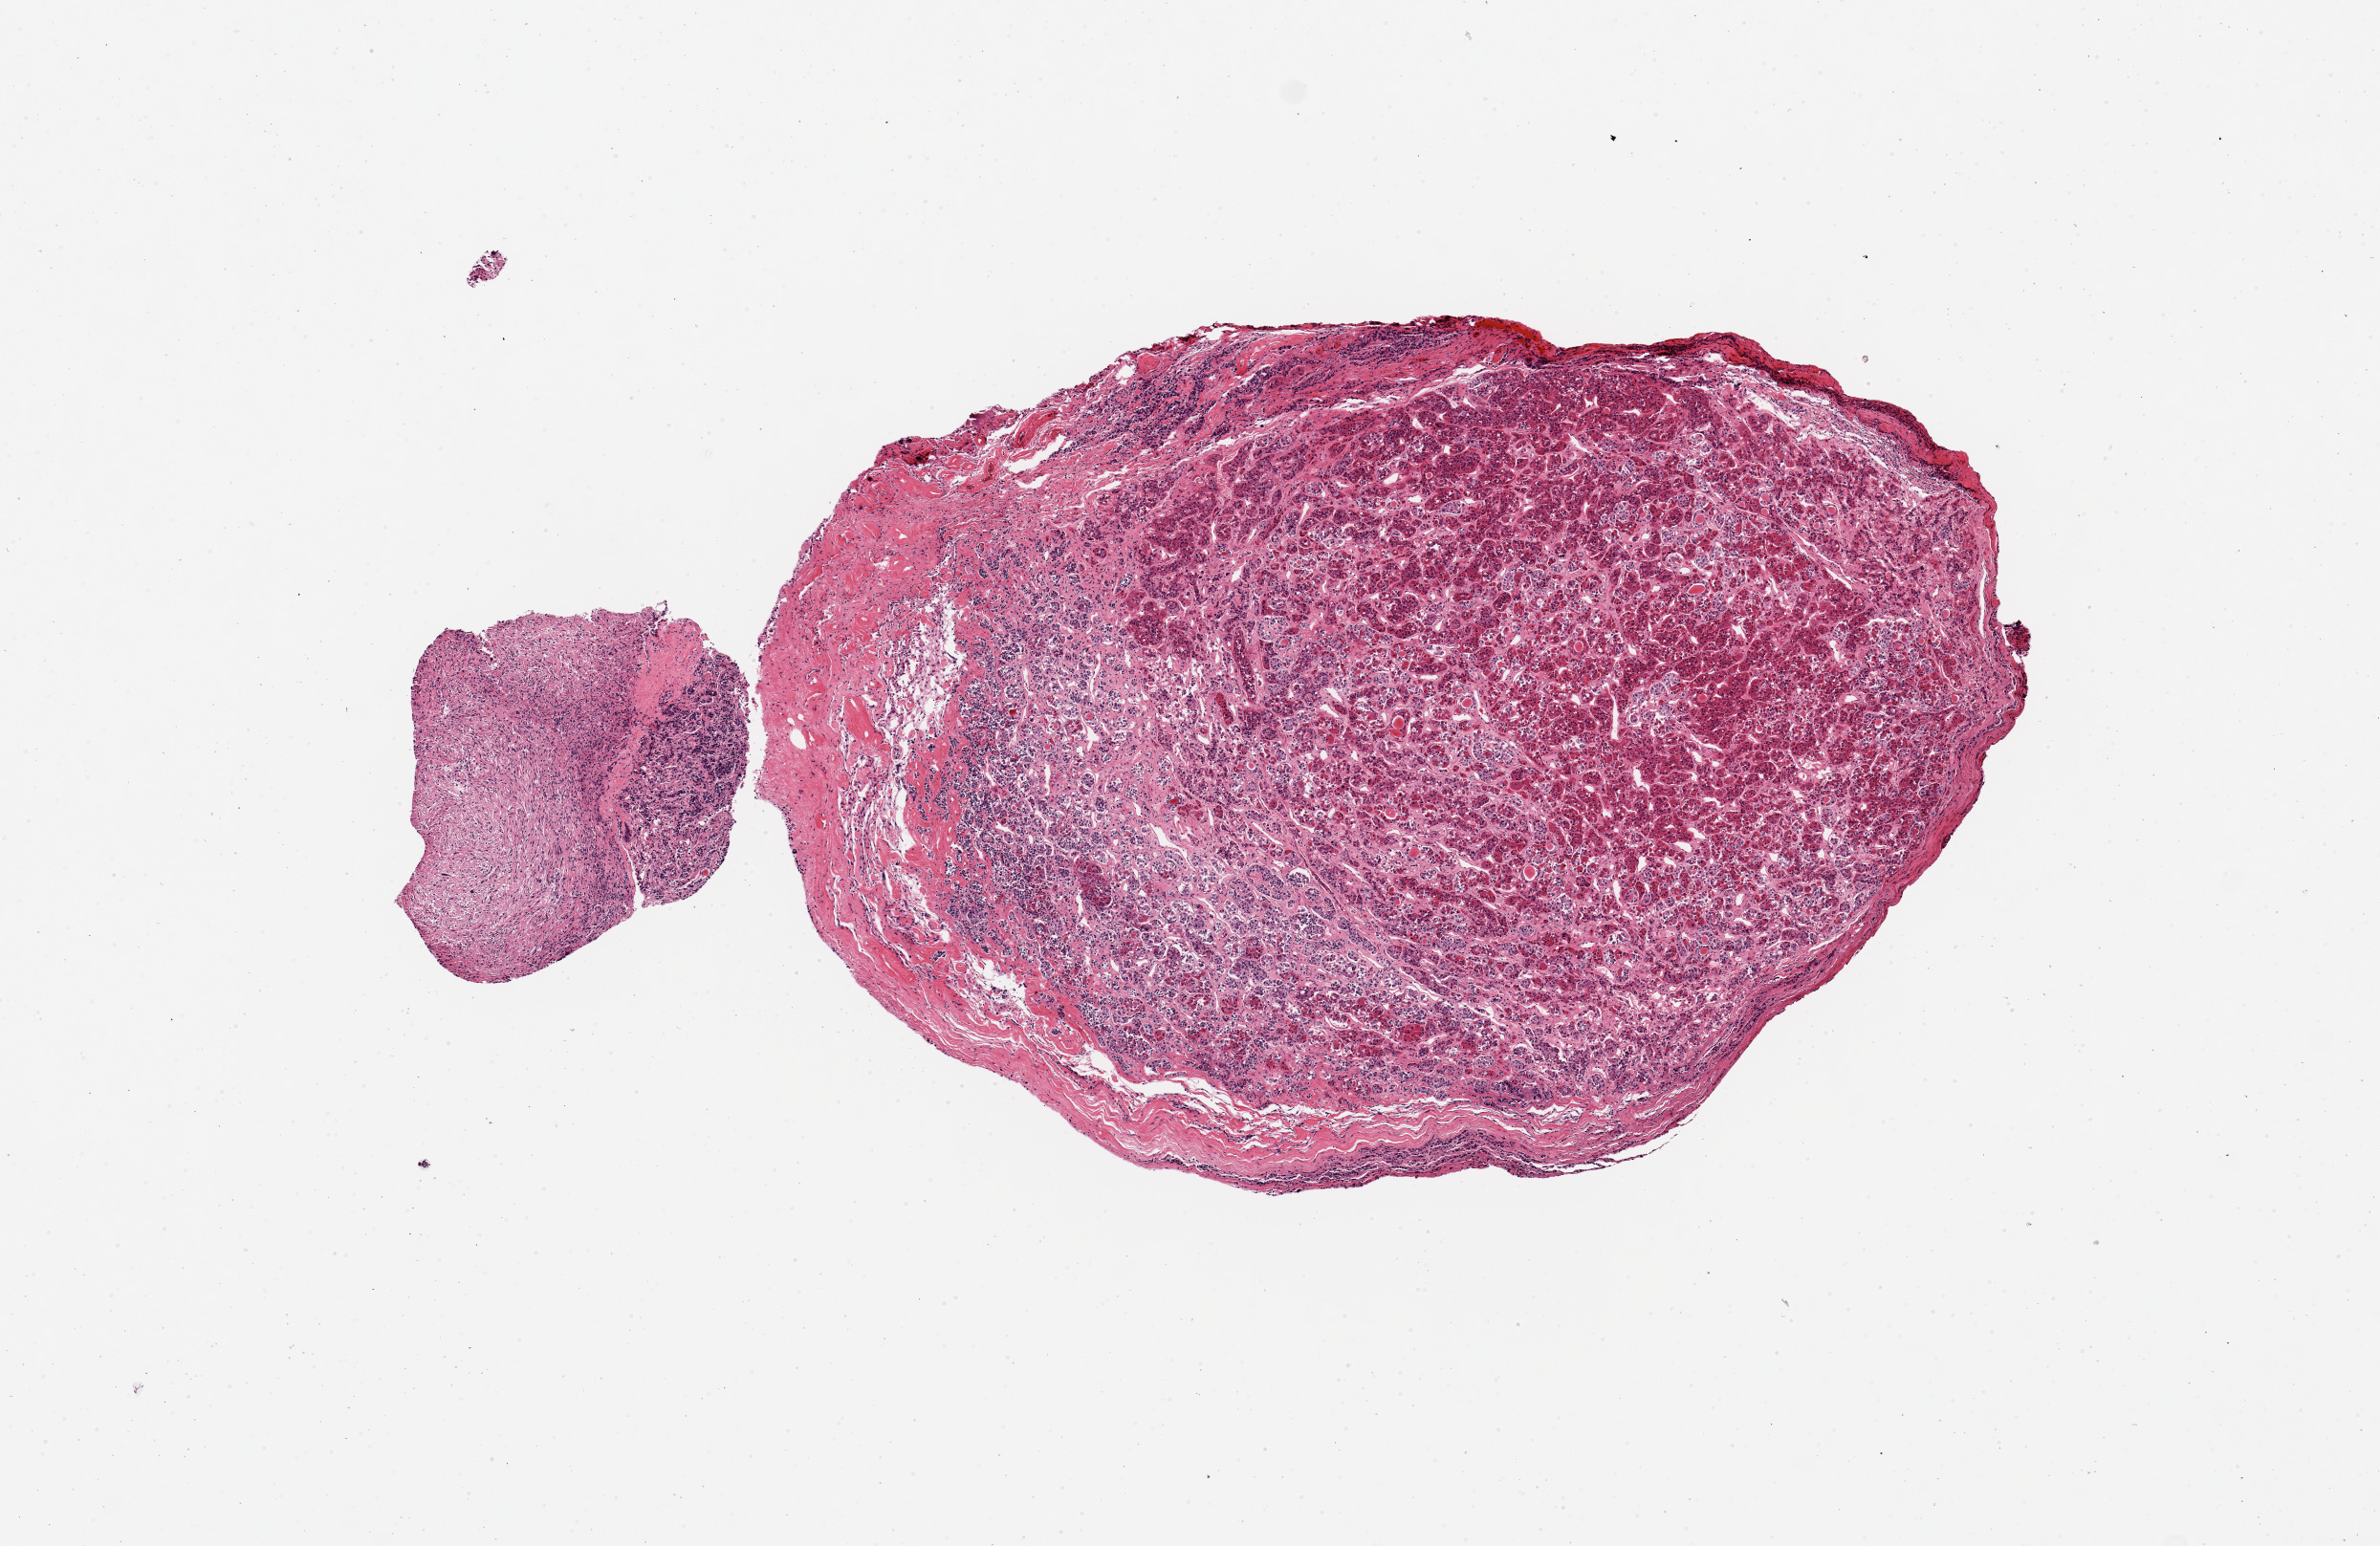
Hematoxylin and eosin (H&E) whole-slide image — low-resolution overview of the scanned area, about 9.8 x 6.4 mm; PAXgene-fixed, paraffin-embedded tissue; section of pituitary (target tissue); tissue donor sample. Donor: male.
Pathologist's review note for this sample: 1 piece adenohypophysis + ~1.5mm fragment of neurohypophysis, no abnormalities.